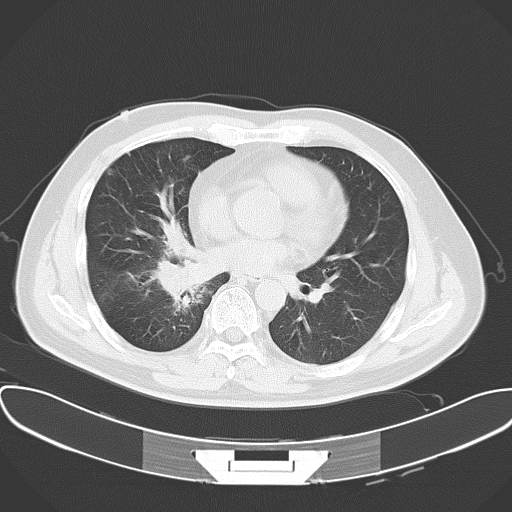
Chest CT, one axial slice; slice 27 of 57 in the series (ordered by position); reconstruction kernel B70f; lung window (W 1500 / L -600 HU); 512 × 512 image matrix, field of view 388 × 388 mm. Patient: male, 48 years. From the clinical record (not read from this slice): clinical TNM (as recorded): T1a N1 M1c; histopathological grade: G3.
Outlined on this slice (bounding box drawn by a radiologist):
- lung tumour (recorded histology: adenocarcinoma): bounding box [x1, y1, x2, y2] px = [155, 221, 213, 299]